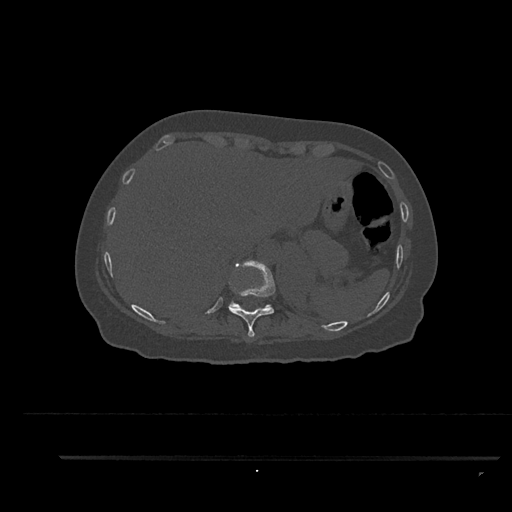
CT including the spine, one axial slice; slice 351 of 797 in the series (ordered by position); reconstruction kernel Br40s/3; 120 kVp; bone window (W 1800 / L 400 HU); 0.5 mm slice thickness; 512 × 512 image matrix, field of view 408 × 408 mm. Female patient, age 44 years. Case-level facts recorded for this patient, not image findings: primary cancer: renal; vertebrae with lytic lesions (as recorded): L1.
Outlined on this slice (semi-automatic segmentation, software-assisted and operator-edited):
- T10 vertebra: box from (x=229, y=260) to (x=275, y=338) px
- T11 vertebra: (x=229, y=300)–(x=271, y=307)